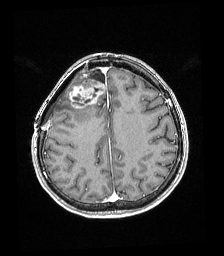
Brain MRI from a brain-tumour surgery series, one axial slice; position 64 of 192 along the scan axis; T1-weighted post-contrast; 224 × 256 image matrix, field of view 219 × 250 mm. Case-level facts recorded for this patient, not image findings: histopathology: Astrocytoma; WHO grade: 4; IDH mutation: yes.
Outlined on this slice (outlined manually by an expert reader):
- tumour: bounding box [x1, y1, x2, y2] px = [68, 81, 104, 109]